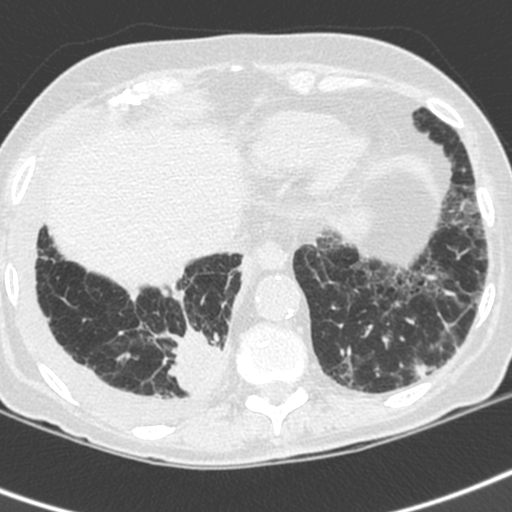
Chest CT (low-dose screening protocol), one axial image, first (baseline) screen, lung window (W 1500 / L -600 HU), 1.3 mm slice thickness, standard (soft-tissue) reconstruction kernel (C), slice 152 of 192 in the series, 512 × 512 image matrix, field of view 288 × 288 mm. Female, age 73 years at enrolment. Current smoker at enrolment.
Expert-annotated lung lesion, bounding box [x1, y1, x2, y2] px = [159, 325, 234, 406]. Screening reader's record for this exam (one nodule recorded; not confirmed to be the boxed lesion): non-calcified nodule or mass ≥4 mm, right lower lobe, 35 × 30 mm, spiculated (stellate) margins, soft tissue attenuation. Later outcome: lung cancer diagnosed 22 days after this screen — adenocarcinoma, NOS, right lower lobe, stage IV (AJCC 6th edition), 35 mm at pathology.